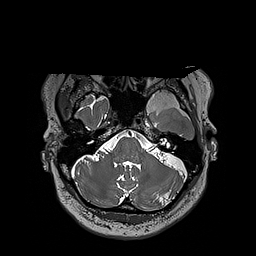
Brain MRI from a brain-tumour surgery series, one axial slice. Position 153 of 192 along the scan axis. 1 mm slice thickness. 256 × 256 image matrix, field of view 250 × 250 mm. From the clinical record (not read from this slice): histopathology: Oligodendroglioma; WHO grade: 3; IDH mutation: yes; tumour location: Left Sylvian Fissure (Temporal).
Annotated regions visible in this slice (outlined manually by an expert reader):
- tumour: box from (x=124, y=91) to (x=197, y=113) px